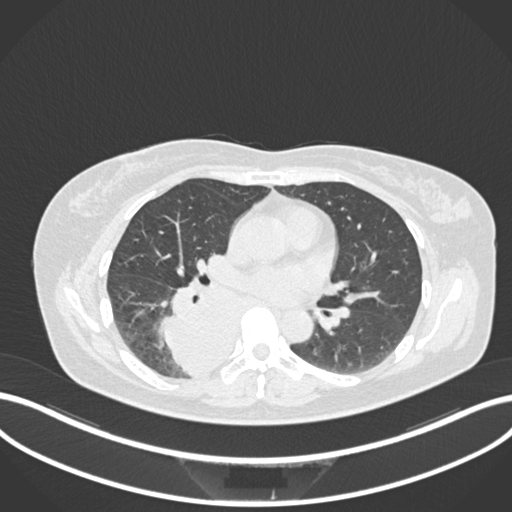
Chest CT, one axial slice. Slice 589 of 677 in the series (ordered by position). Reconstruction kernel B30f. Lung window (W 1500 / L -600 HU). 512 × 512 image matrix. Patient: female, 54 years. Case-level facts recorded for this patient, not image findings: clinical TNM (as recorded): T4 N0 M0.
Annotated regions visible in this slice (rectangle marked by the reading radiologist):
- lung tumour (recorded histology: adenocarcinoma): box from (x=160, y=277) to (x=248, y=383) px